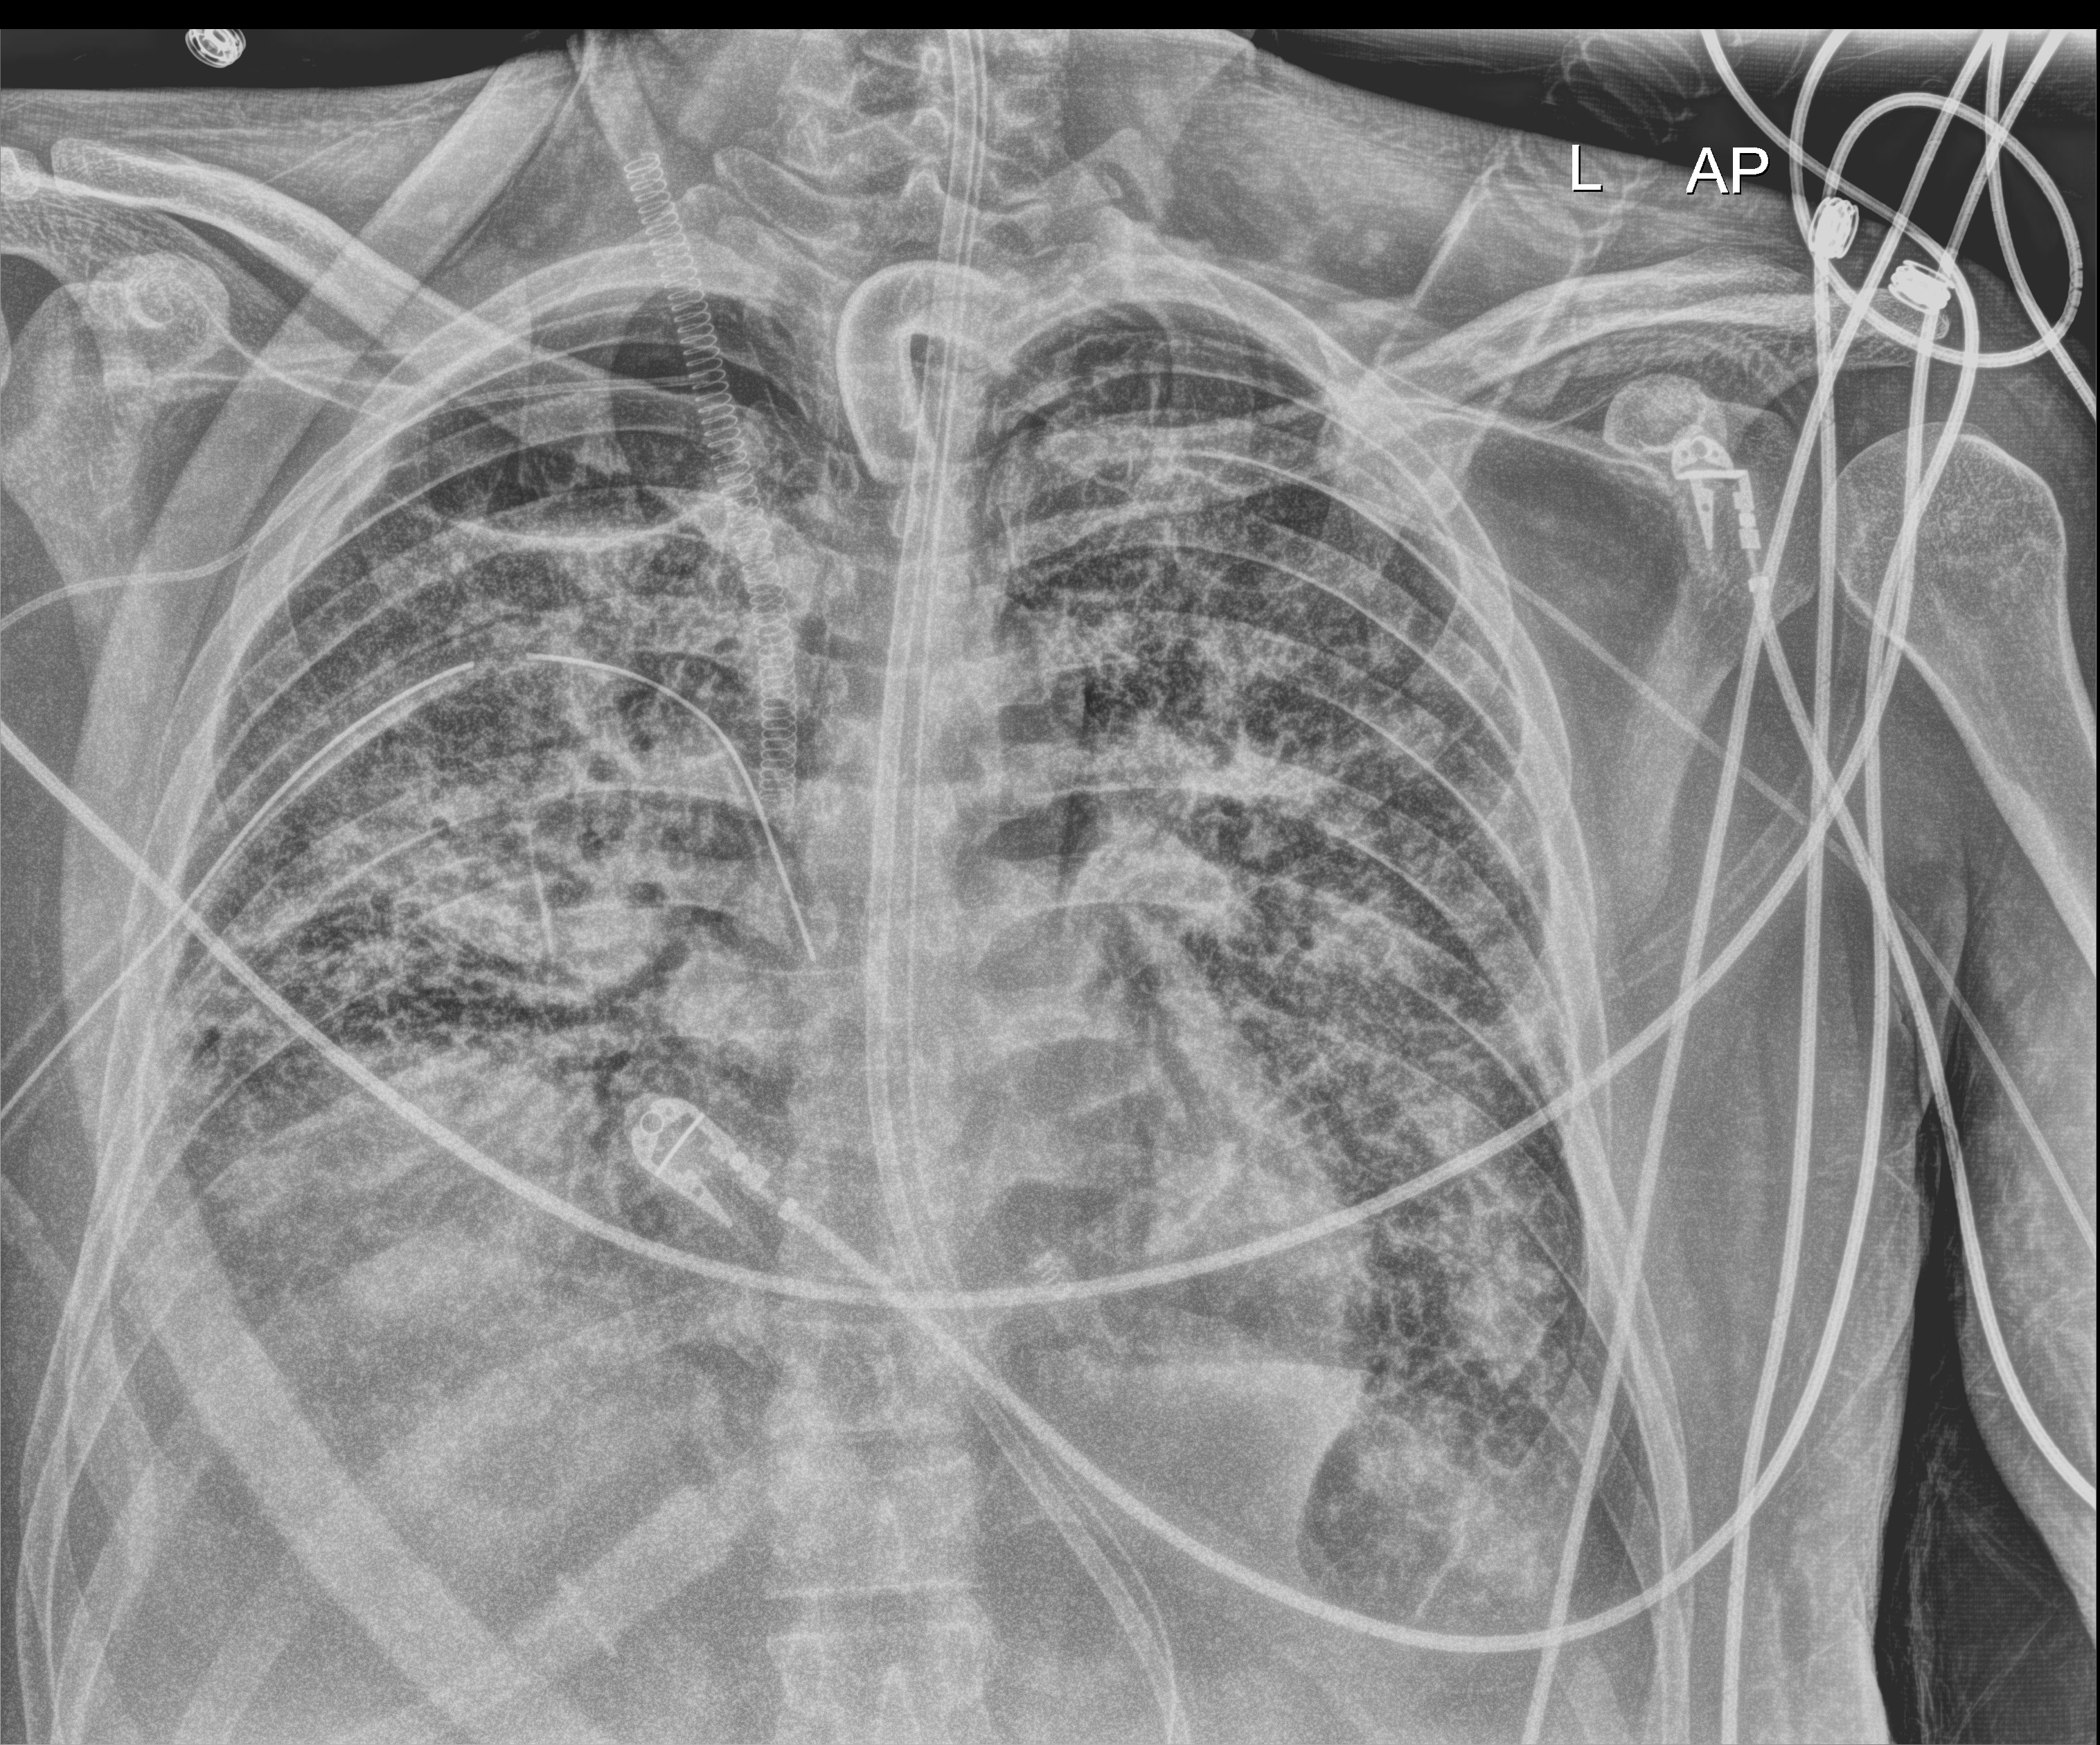
Chest radiograph (digital radiography), anteroposterior (AP) projection. Patient hospitalised with COVID-19, aged 18–59 years.
Admission-level facts for this patient (not findings on this image; timing relative to this image not recorded):
- mechanically ventilated during this hospital stay: yes